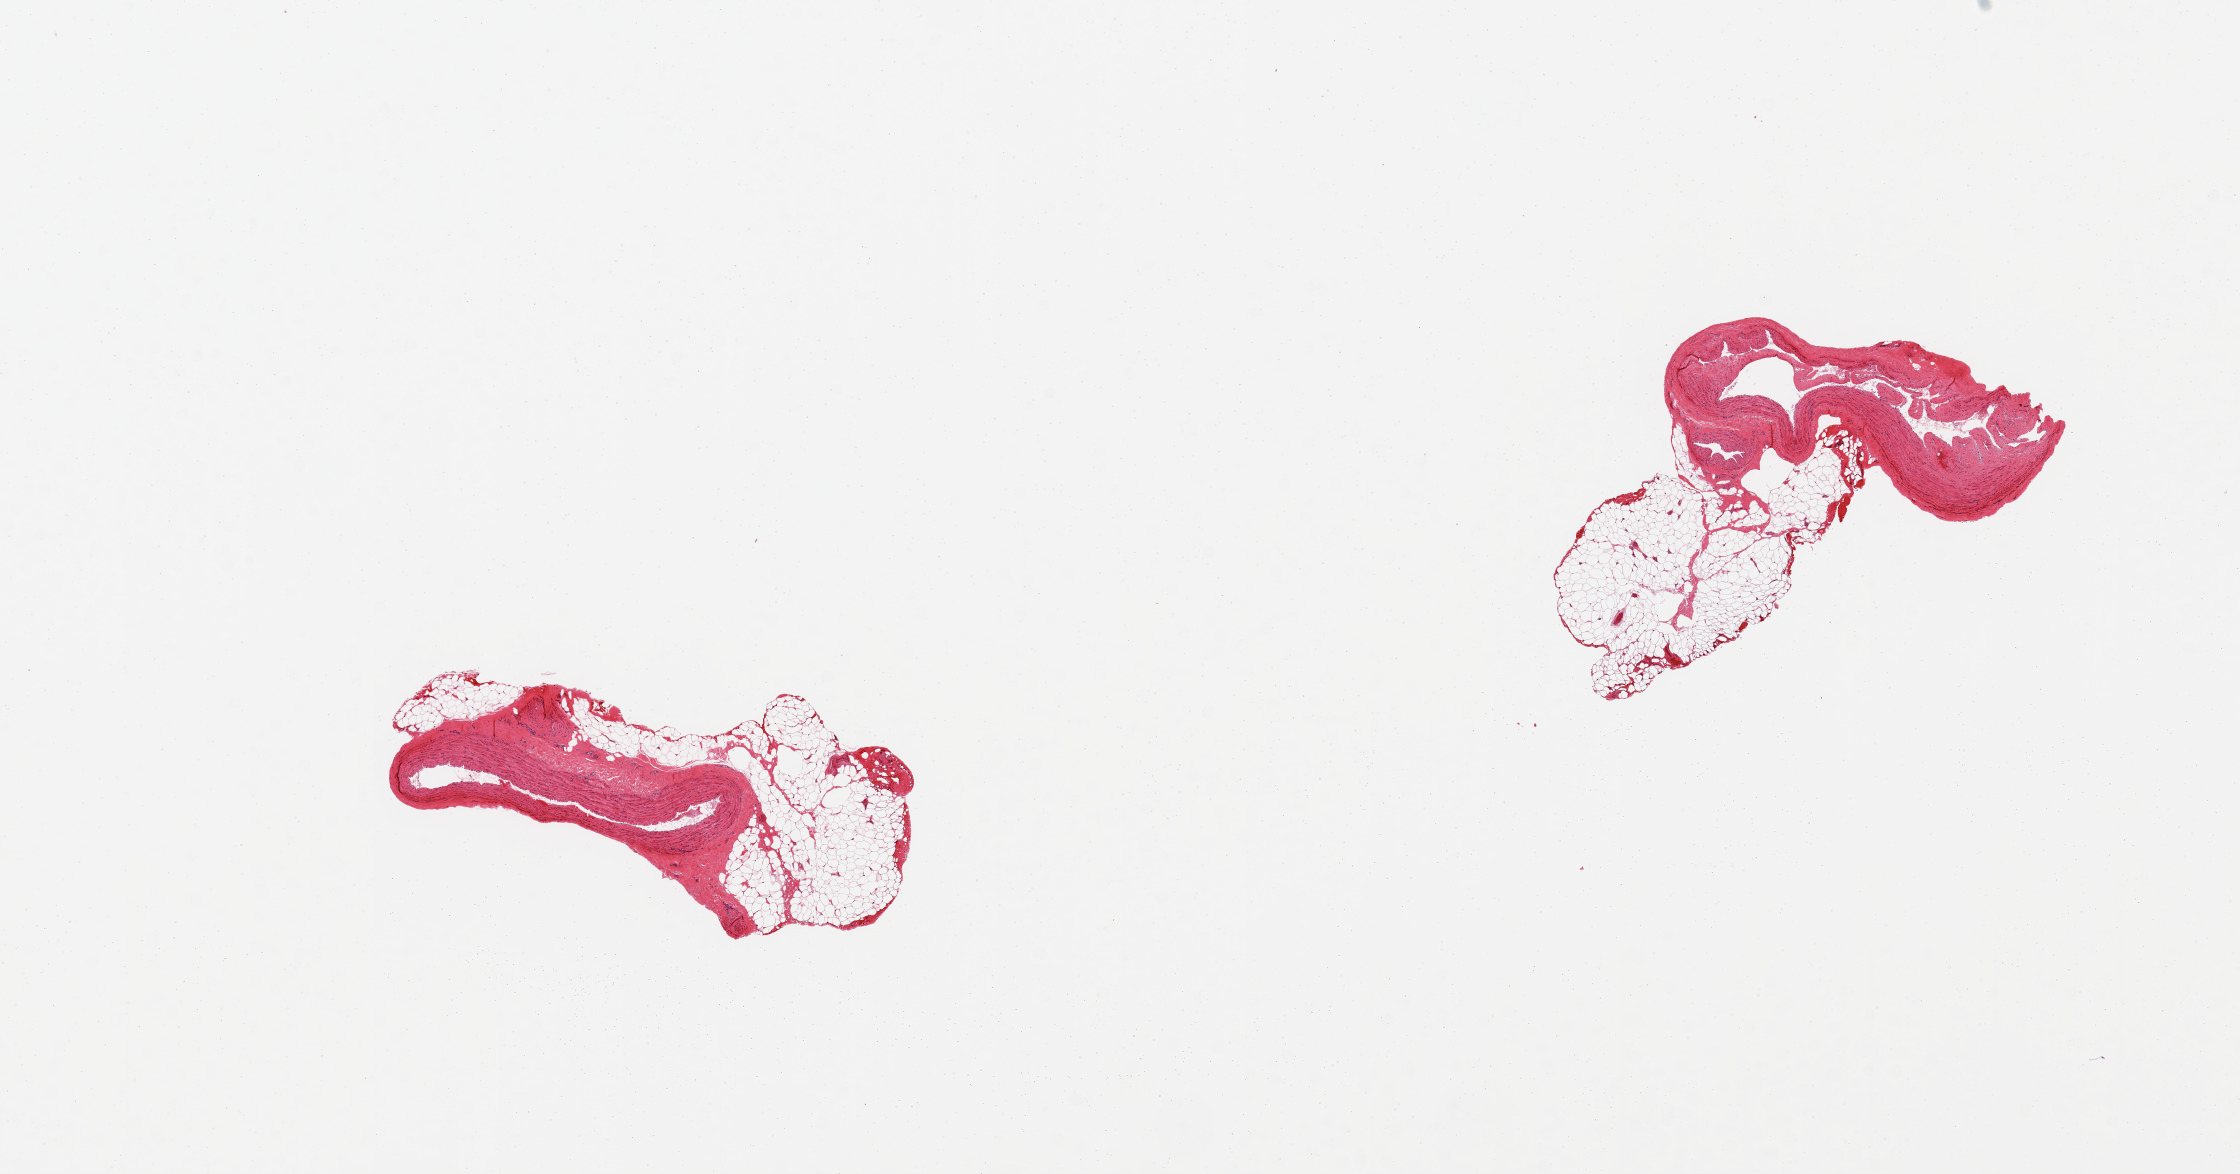
Whole-slide image, H&E stain — shown as a low-resolution overview of the whole scanned area (about 17.7 x 9.3 mm). PAXgene-fixed, paraffin-embedded tissue. Section of coronary artery (target tissue). Donor tissue sample. Donor sex: male.
• reviewer comment on this tissue sample: 2 pieces; excessive adherent fat (50% of specimen)